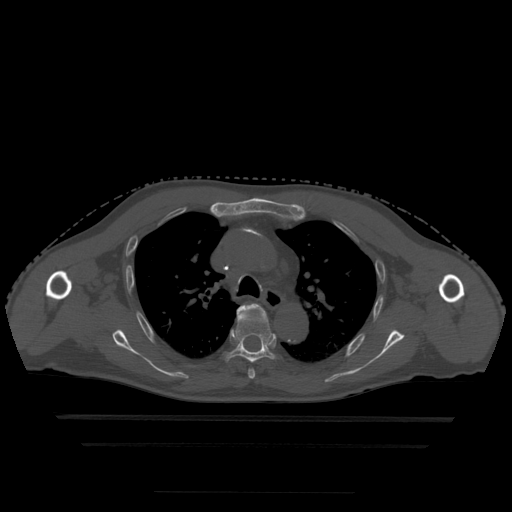
CT including the spine, one axial slice. Slice 340 of 522 in the series (ordered by position). Bone window (W 1800 / L 400 HU). 1.25 mm slice thickness. 512 × 512 image matrix. Patient age 68 years. From the clinical record (not read from this slice): primary cancer: urothelial.
Outlined on this slice (semi-automatically segmented with operator editing):
- T4 vertebra: box from (x=237, y=304) to (x=263, y=379) px
- T5 vertebra: (x=228, y=307)–(x=274, y=364)